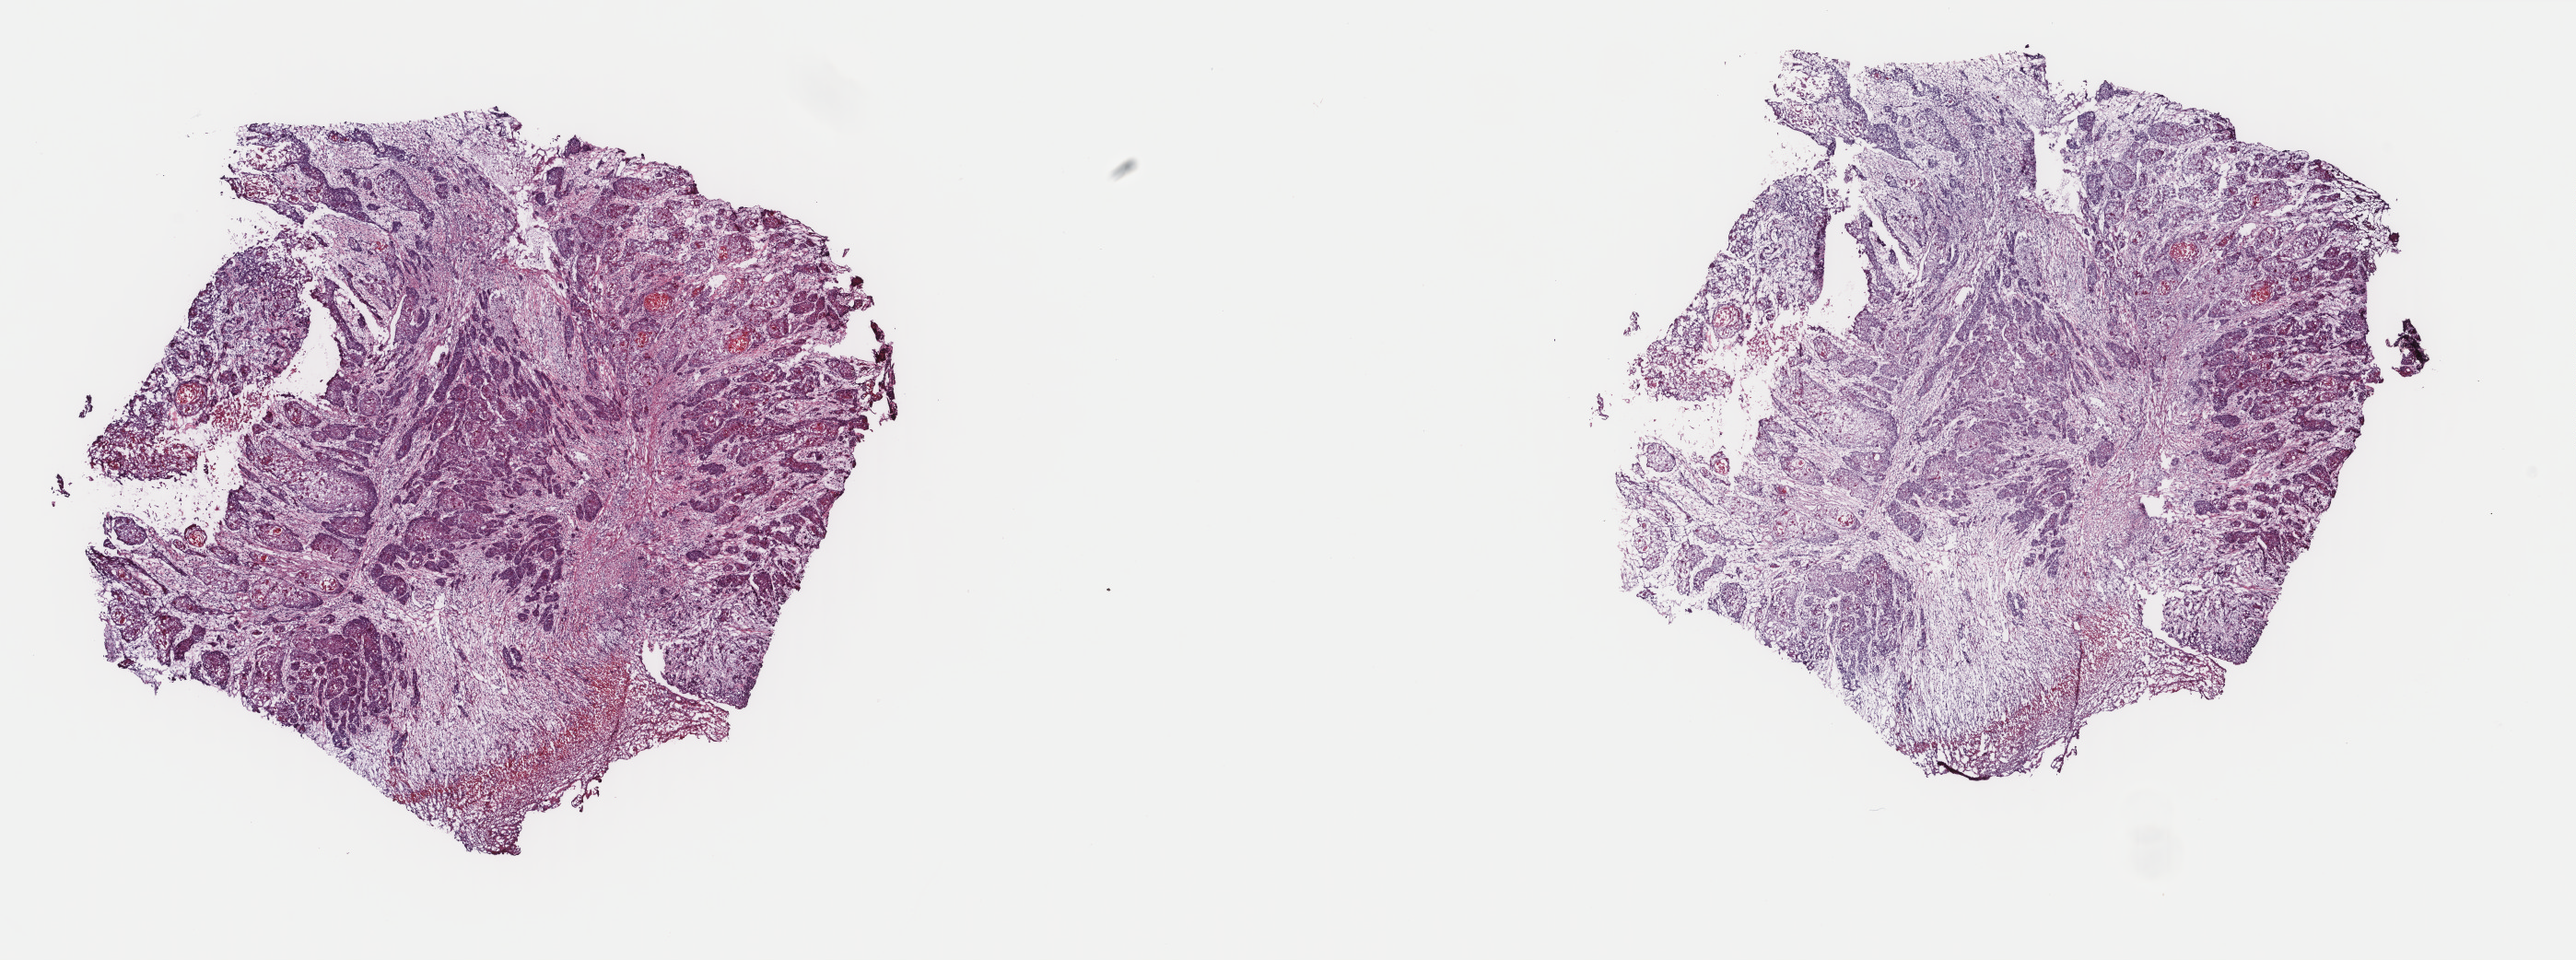
Digitized Hematoxylin and eosin (H&E) stained tissue section (whole slide) — low-resolution overview of the scanned area, about 22.2 x 8.3 mm. Frozen section. Sample: primary tumour, head and neck. Female patient; age at initial diagnosis 61 years. Histologic grade: G2 (moderately differentiated). Slide review estimates, as recorded: tumour cells 100%, tumour nuclei 70%, normal cells 0%, stromal cells 0%, necrosis 0%. Infiltration values recorded for this section: lymphocyte infiltration 3%, monocyte infiltration 0%, neutrophil infiltration 0%.
TNM: T4a N2b MX. AJCC pathologic stage: IVA (7th edition). Diagnosis: Squamous cell carcinoma, NOS (tongue, NOS). Laterality: left.